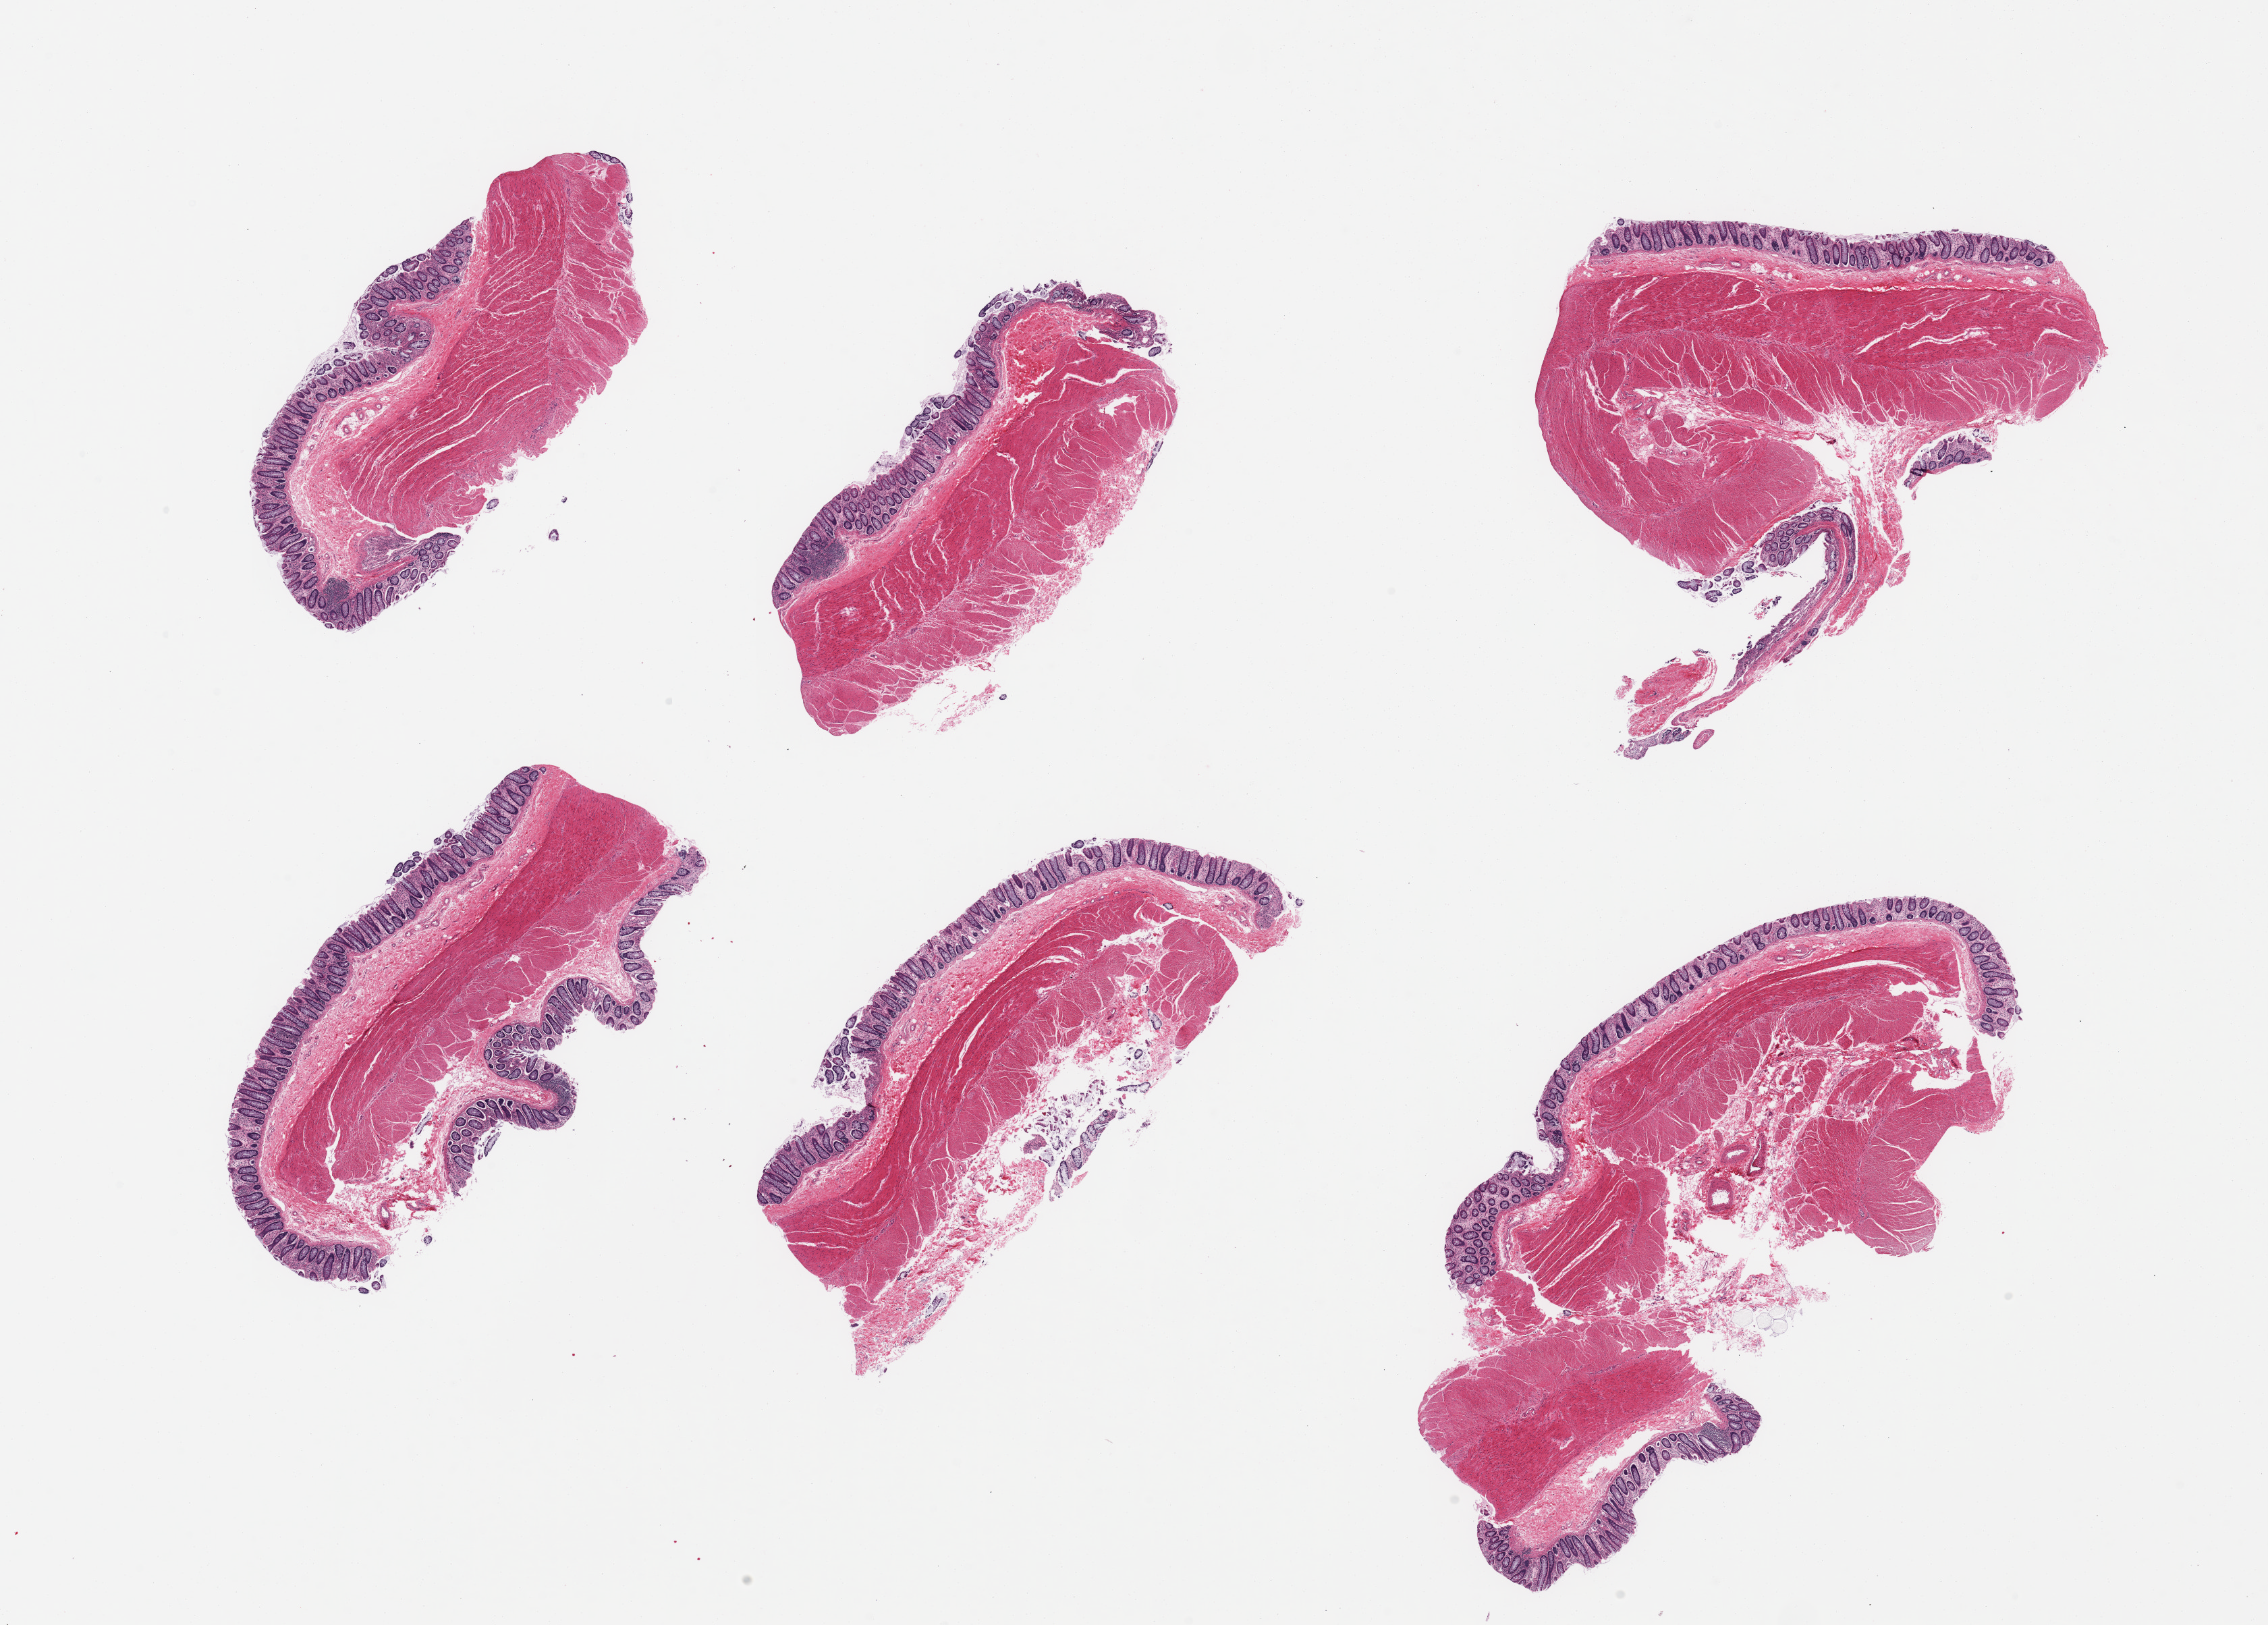
Digitized haematoxylin and eosin-stained section, a low-resolution overview of the entire scanned area, about 26.6 x 19.0 mm (acquisition: 20x scan). Donor sex: female.
• specimen: PAXgene-fixed, paraffin-embedded tissue; target tissue: sigmoid colon; tissue donor sample